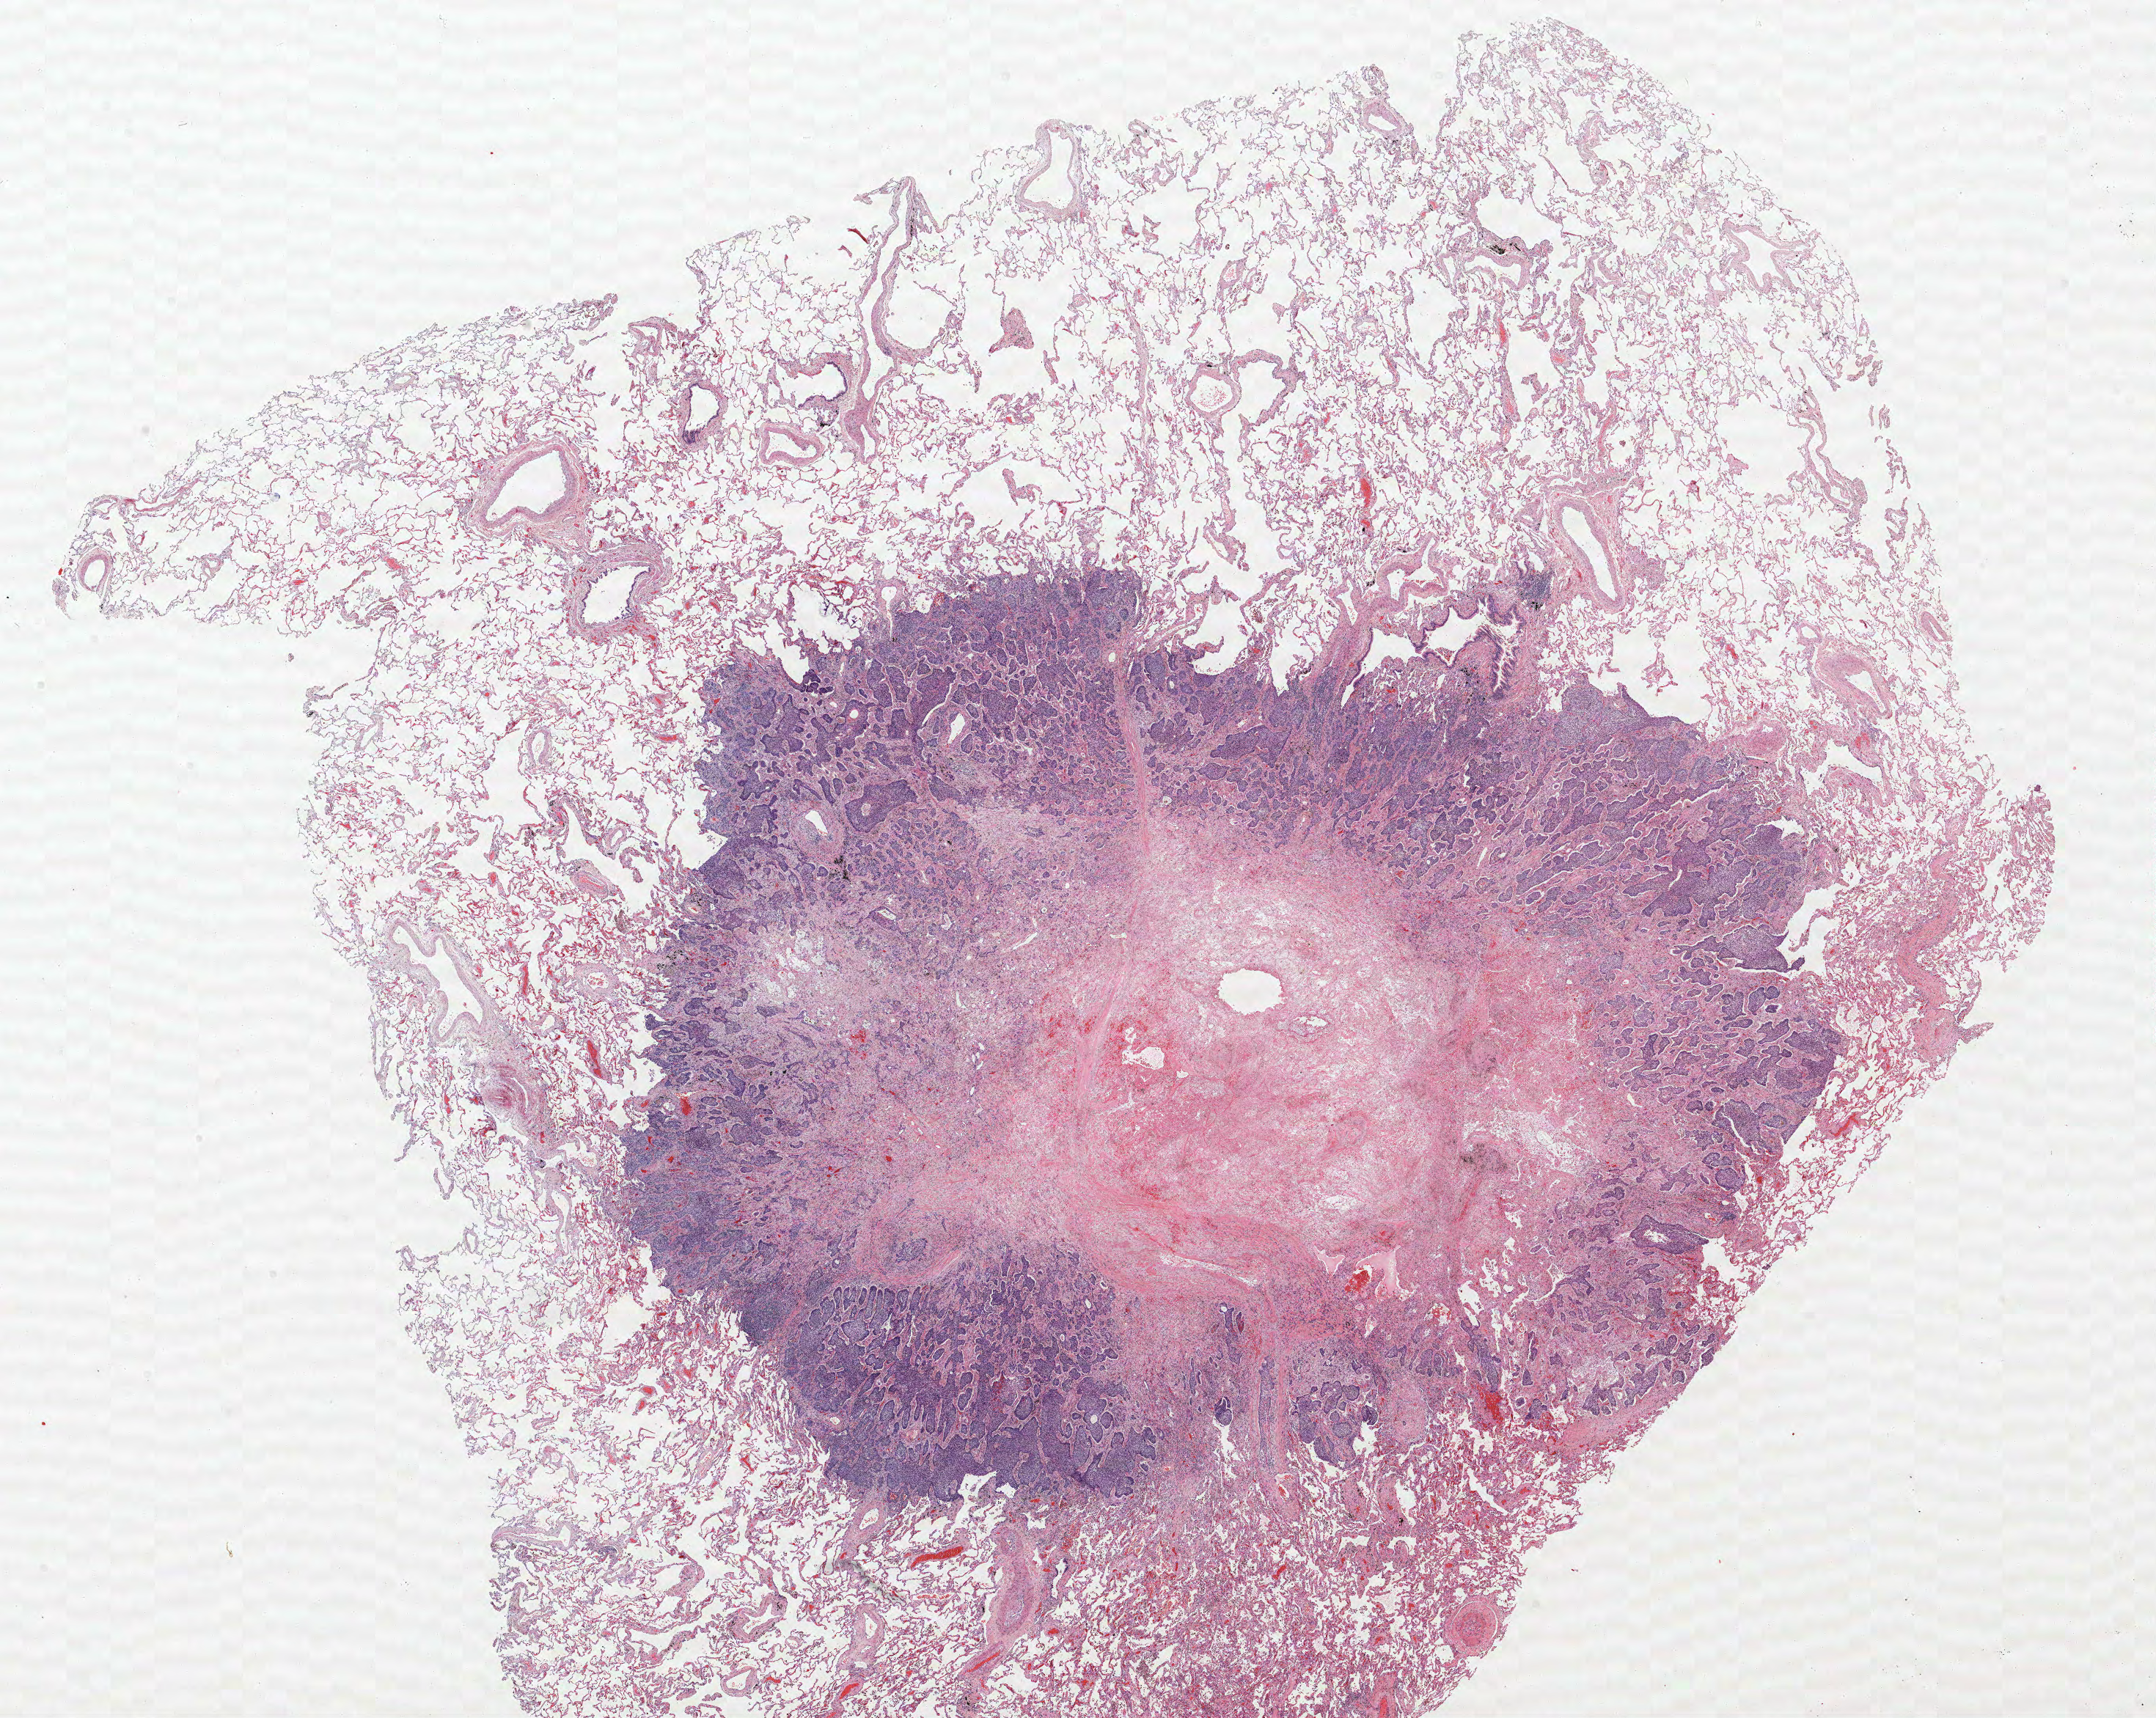
H&E-stained whole-slide image, low-resolution overview of the scanned area, about 23.5 x 18.7 mm (from a 40x scan), FFPE section, lung. Male, age 70 at enrolment. Current smoker at enrolment. Grade: poorly differentiated (G3).
Primary tumour location (clinical record): right upper lobe. Participant's lung-cancer diagnosis: Large cell neuroendocrine carcinoma. Tumour size (pathology): 15 mm. Stage (AJCC 6th edition): IA. ICD-O-3 topography: upper lobe of lung (C34.1).